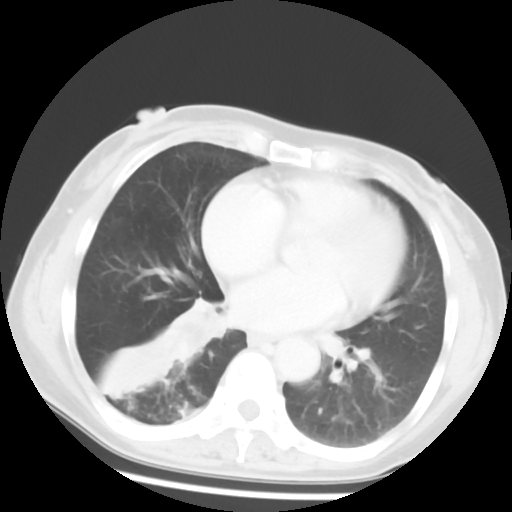
Chest CT, one axial slice. Position 24 of 52 along the scan axis. Lung window (W 1500 / L -600 HU). 512 × 512 image matrix, field of view 297 × 297 mm. Patient: female, 54 years. Case-level facts recorded for this patient, not image findings: clinical TNM (as recorded): T1c N0 M0; histopathological grade: G1-2.
Structures marked on this image (rectangle marked by the reading radiologist):
- lung tumour (recorded histology: squamous cell carcinoma): box from (x=162, y=290) to (x=231, y=360) px